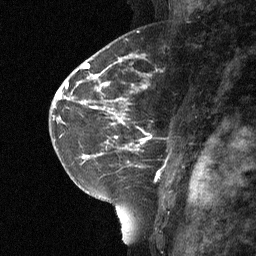
Breast MRI (dynamic contrast-enhanced), one sagittal slice. Position 40 of 64 along the scan axis. Dynamic contrast-enhanced study with each time point stored as its own series, time point 2 of 3 at this slice position (early post-contrast, ordered by acquisition time). 1.5 T. TE 4.8 ms, TR 27 ms. 2 mm slice thickness. 256 × 256 image matrix, field of view 180 × 180 mm. Female patient, age 42 years. Case-level facts recorded for this patient, not image findings: setting: breast cancer imaged before/during neoadjuvant chemotherapy; receptor status: triple-negative.
Outlined on this slice (semi-automatic segmentation, software-assisted and operator-edited):
- analysis volume of interest (the breast-tissue region the enhancement analysis was run in; not a lesion): box from (x=115, y=85) to (x=190, y=160) px
- tumour enhancement mask (voxels above the 90 % enhancement threshold inside the analysis volume of interest): (x=115, y=86)–(x=146, y=151)